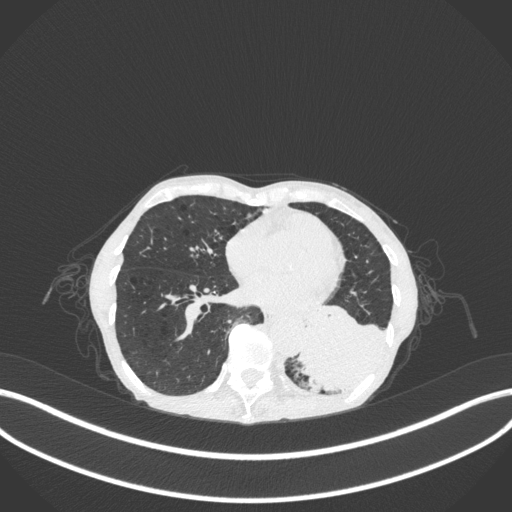
Chest CT, one axial slice. Slice 98 of 347 in the series (ordered by position). Reconstruction kernel B31f. 120 kVp. Lung window (W 1500 / L -600 HU). 1 mm slice thickness. 512 × 512 image matrix, field of view 400 × 400 mm. Female patient, age 70 years. Case-level facts recorded for this patient, not image findings: clinical TNM (as recorded): T3 N0 M0.
Annotated regions visible in this slice (rectangle marked by the reading radiologist):
- lung tumour (recorded histology: small cell carcinoma): bounding box (x1, y1, x2, y2) in pixels: (293, 296, 392, 393)